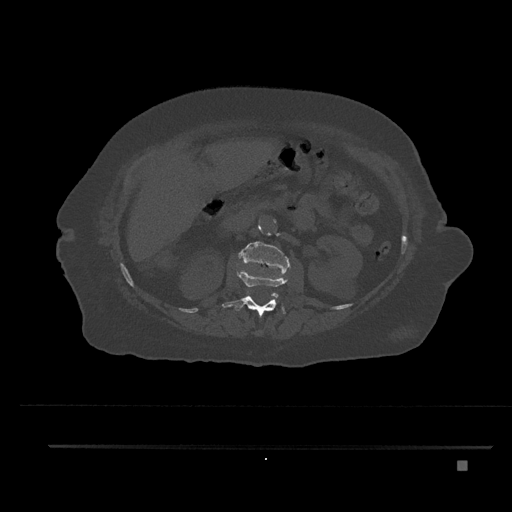
CT including the spine, one axial slice; slice 210 of 797 in the series (ordered by position); reconstruction kernel Br40s/3; bone window (W 1800 / L 400 HU); 512 × 512 image matrix, field of view 437 × 437 mm. Female patient, age 76 years. Case-level facts recorded for this patient, not image findings: primary cancer: lung.
Outlined on this slice (semi-automatic segmentation, software-assisted and operator-edited):
- L1 vertebra: bounding box [x1, y1, x2, y2] px = [222, 270, 289, 318]
- L2 vertebra: [239, 241, 291, 297]